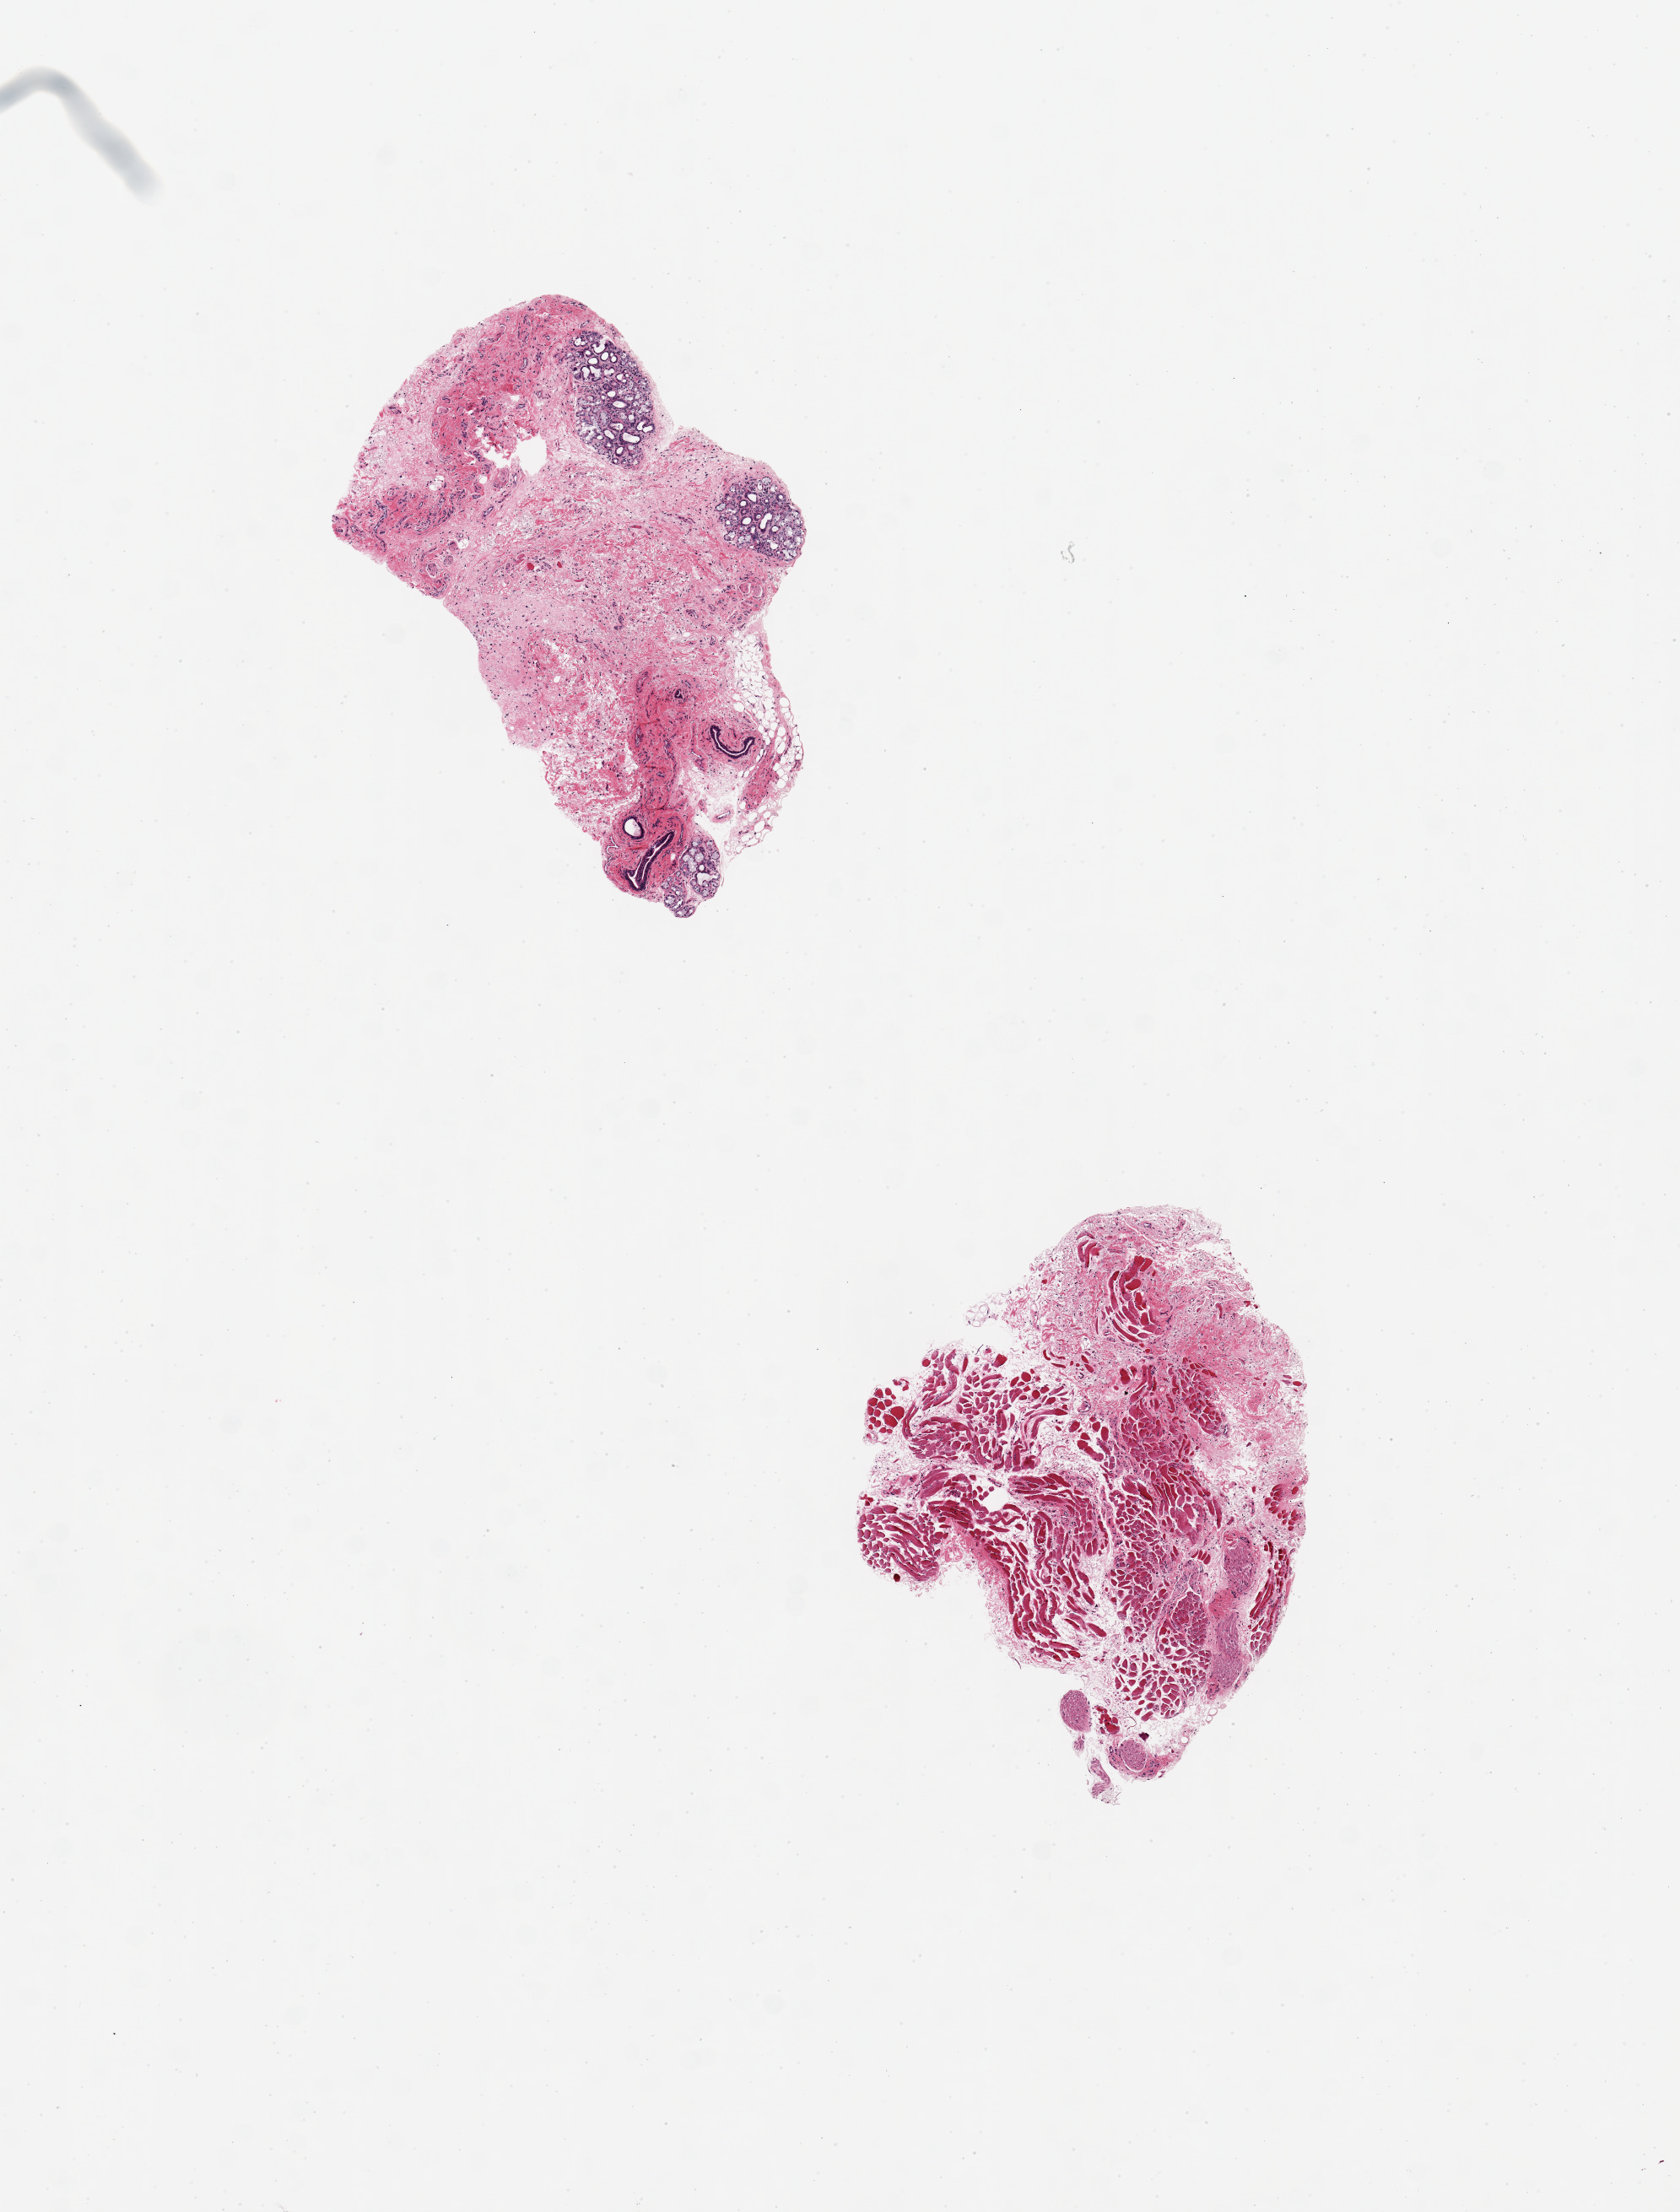
Whole-slide image, haematoxylin and eosin stain, brightfield — low-resolution overview of the scanned area, about 7.9 x 10.4 mm; PAXgene-fixed paraffin-embedded (PFPE) section; sampled site (target tissue): minor salivary gland; donor tissue sample.
• reviewer comment on this tissue sample: 2 pieces, 3x2 & 2x2mm; 1 w/ 3, 0.5mm salivary glands; other no glands, only muscle and nerves